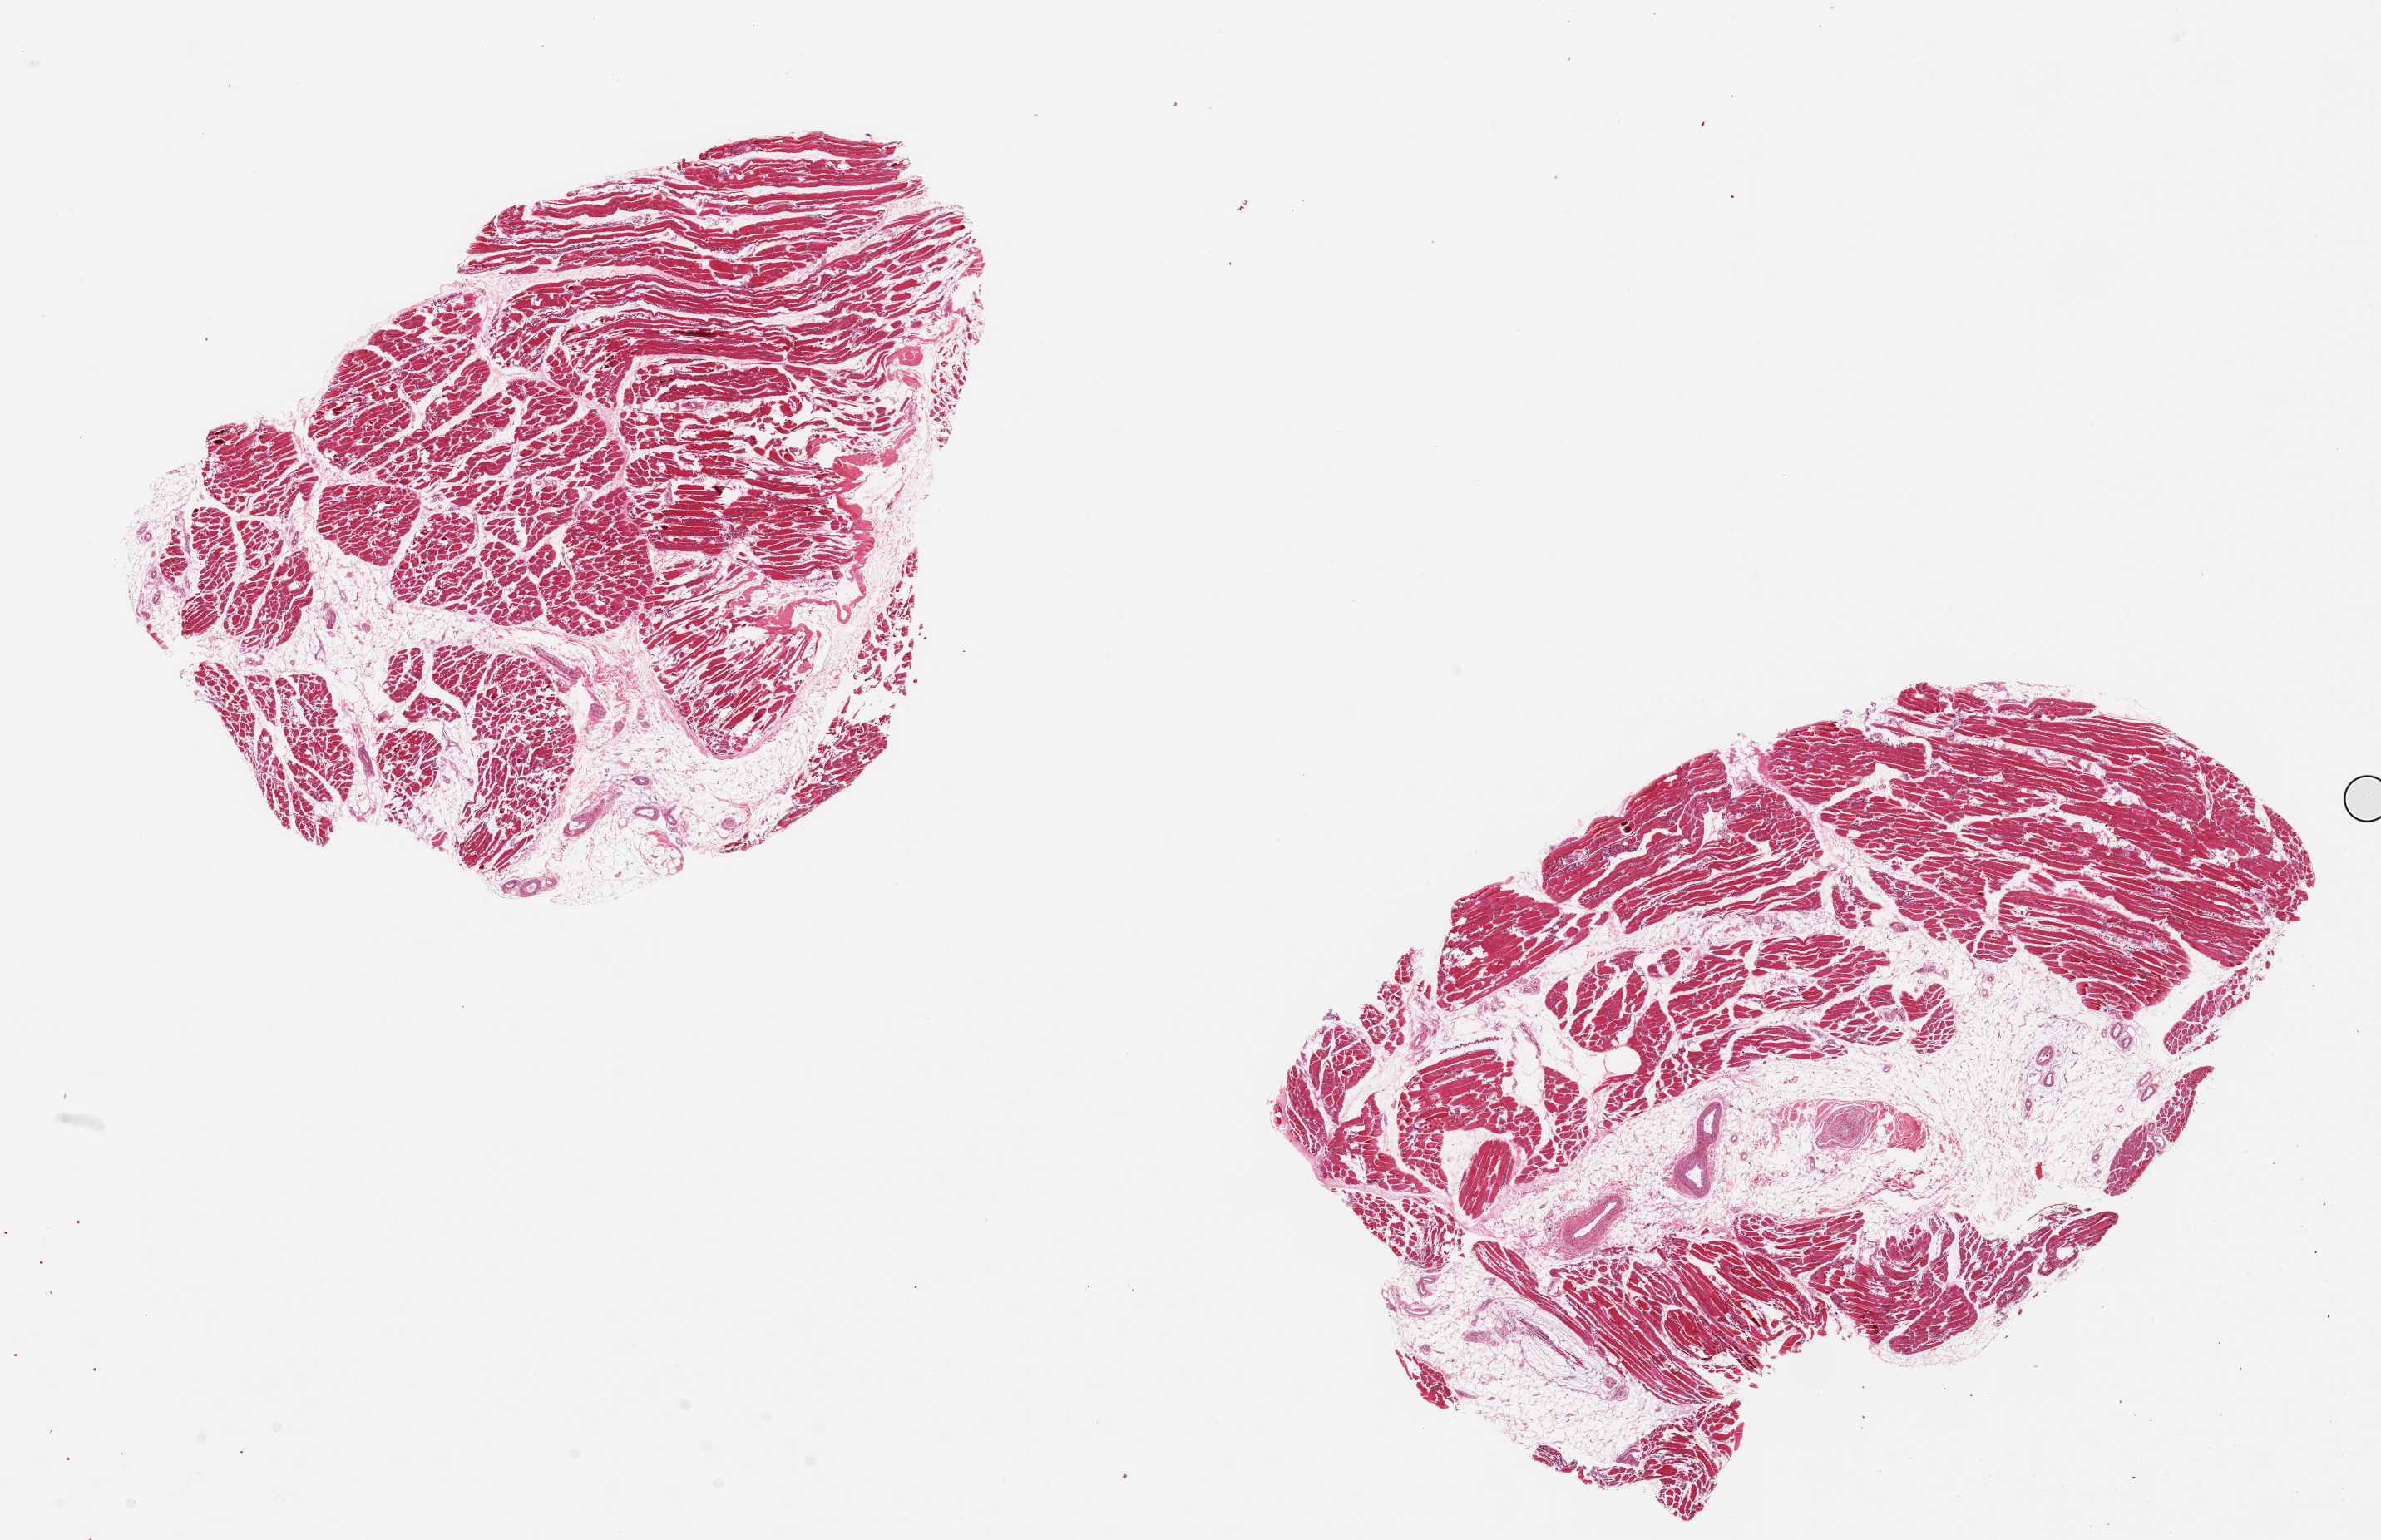
H&E whole-slide image — whole scanned area (about 22.6 x 14.6 mm, from a 20x scan) shown as a low-resolution overview; PAXgene-fixed, paraffin-embedded tissue; sampled site (target tissue): skeletal muscle; donor tissue sample. Donor sex: male.
Reviewer comment on this tissue sample: 2 pieces, ~9x6mm, ~40% intermingled f.